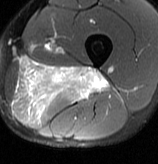
MRI of an extremity soft-tissue mass, one axial slice; position 33 of 70 along the scan axis; T2-weighted fat-saturated; MR volume resampled by the dataset authors to the PET/CT grid (not the native acquisition matrix); 3.27 mm slice thickness; 158 × 164 image matrix, field of view 154 × 160 mm. Male patient. Case-level facts recorded for this patient, not image findings: histological type: extraskeletal osteosarcoma; grade: high; site of the primary tumour: left adductur.
Annotated regions visible in this slice (expert contour drawn on MRI and transferred to this co-registered scan by the dataset authors):
- gross tumour volume (mass): box from (x=10, y=57) to (x=110, y=125) px